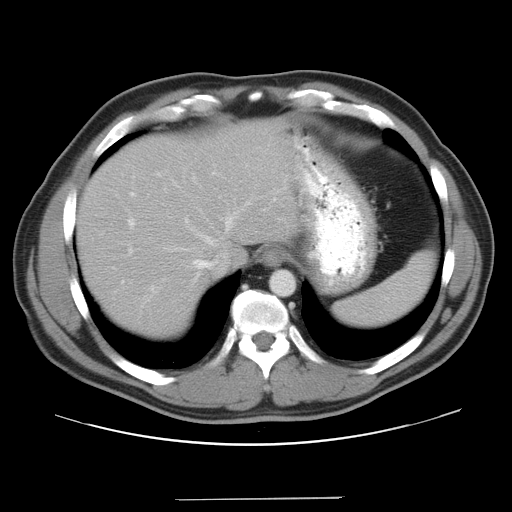
Contrast-enhanced abdominal CT, one axial slice. Position 32 of 37 along the scan axis. Reconstruction kernel STANDARD. 120 kVp. Intravenous contrast given. Soft-tissue window (W 400 / L 40 HU). 7.5 mm slice thickness. 512 × 512 image matrix. Male patient, age 46 years. From the clinical record (not read from this slice): diagnosis: colorectal cancer liver metastases, imaged before liver resection; multiple liver metastases: yes; largest metastasis: 1 cm; chemotherapy before resection: yes.
Annotated regions visible in this slice (expert manual segmentation):
- hepatic veins: bounding box <163,158,266,280> (left, top, right, bottom; pixels)
- liver: <79,126,290,334>
- planned liver remnant (the part of the liver to remain after resection): <79,126,290,333>
- portal vein (with intrahepatic branches): <128,172,195,229>
- liver metastasis: <245,230,259,241>